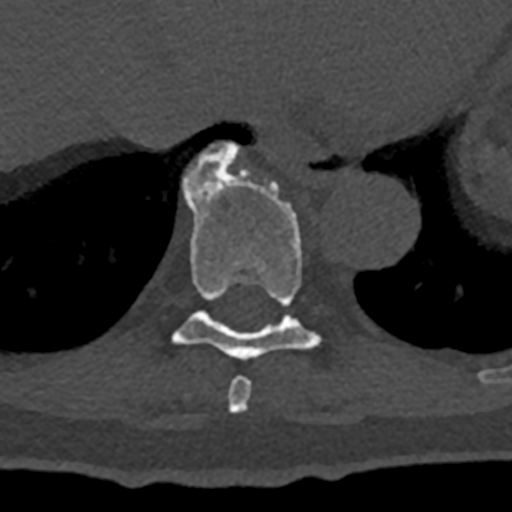
CT including the spine, one axial slice; position 655 of 797 along the scan axis; reconstruction kernel Br40s/3; 120 kVp; bone window (W 1800 / L 400 HU); 512 × 512 image matrix. Male patient, age 74 years. Case-level facts recorded for this patient, not image findings: primary cancer: renal; vertebrae with lytic lesions (as recorded): T10, L1, L2, L3, L4, L5.
Outlined on this slice (semi-automatically segmented with operator editing):
- T10 vertebra: box from (x=184, y=142) to (x=240, y=181) px
- T8 vertebra: (x=228, y=376)–(x=252, y=414)
- T9 vertebra: (x=172, y=145)–(x=322, y=360)